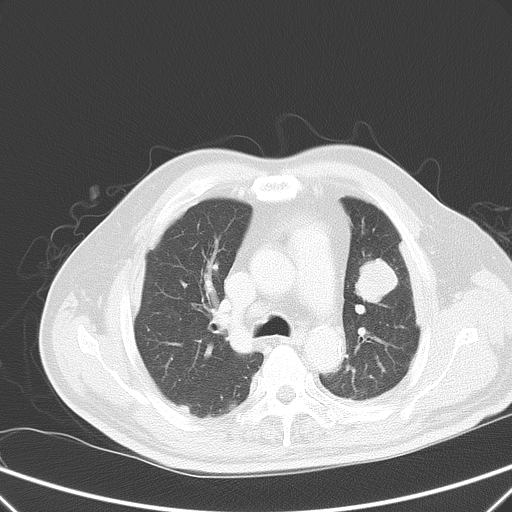
Chest CT, one axial slice. Position 40 of 59 along the scan axis. 120 kVp. Intravenous contrast given. Lung window (W 1500 / L -600 HU). 5 mm slice thickness. 512 × 512 image matrix, field of view 357 × 357 mm. Patient: male, 66 years. Case-level facts recorded for this patient, not image findings: clinical TNM (as recorded): T1c N3 M1a.
Outlined on this slice (rectangle marked by the reading radiologist):
- lung tumour (recorded histology: squamous cell carcinoma): box from (x=350, y=257) to (x=404, y=307) px